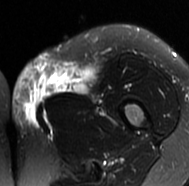
MRI of an extremity soft-tissue mass, one axial slice. Position 26 of 77 along the scan axis. T2-weighted fat-saturated. MR volume resampled by the dataset authors to the PET/CT grid (not the native acquisition matrix). 189 × 186 image matrix, field of view 185 × 182 mm. Female patient. Case-level facts recorded for this patient, not image findings: histological type: leiomyosarcoma; grade: high; site of the primary tumour: groin.
Outlined on this slice (expert contour drawn on MRI and transferred to this co-registered scan by the dataset authors):
- gross tumour volume including surrounding oedema: bounding box [x1, y1, x2, y2] px = [10, 52, 96, 130]
- gross tumour volume (mass): [65, 70, 93, 91]